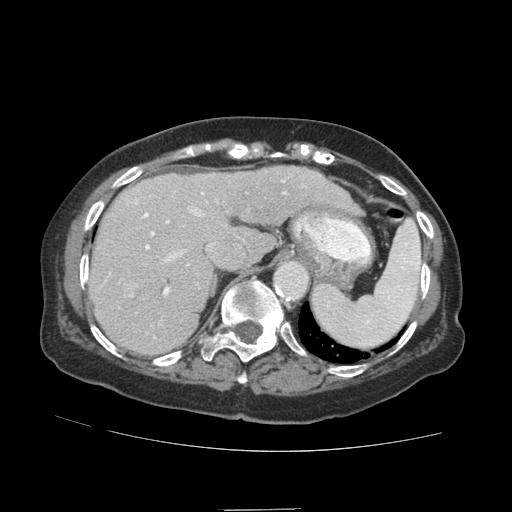
Contrast-enhanced abdominal CT (liver protocol), one axial slice; slice 67 of 89 in the series (ordered by position); 140 kVp; soft-tissue window (W 400 / L 40 HU); 2.5 mm slice thickness; 512 × 512 image matrix. Case-level facts recorded for this patient, not image findings: diagnosis: hepatocellular carcinoma (patient treated with transarterial chemoembolisation; whether this scan precedes or follows treatment is not stated here); TNM stage (as recorded): Stage-II; Child-Pugh class: A.
Outlined on this slice (semi-automatic segmentation, software-assisted and operator-edited):
- liver parenchyma outside the tumour (the mass and vessels are separate outlines, so this box may not span the whole liver): bounding box [x1, y1, x2, y2] px = [88, 166, 306, 354]
- liver vessels: [104, 177, 287, 338]